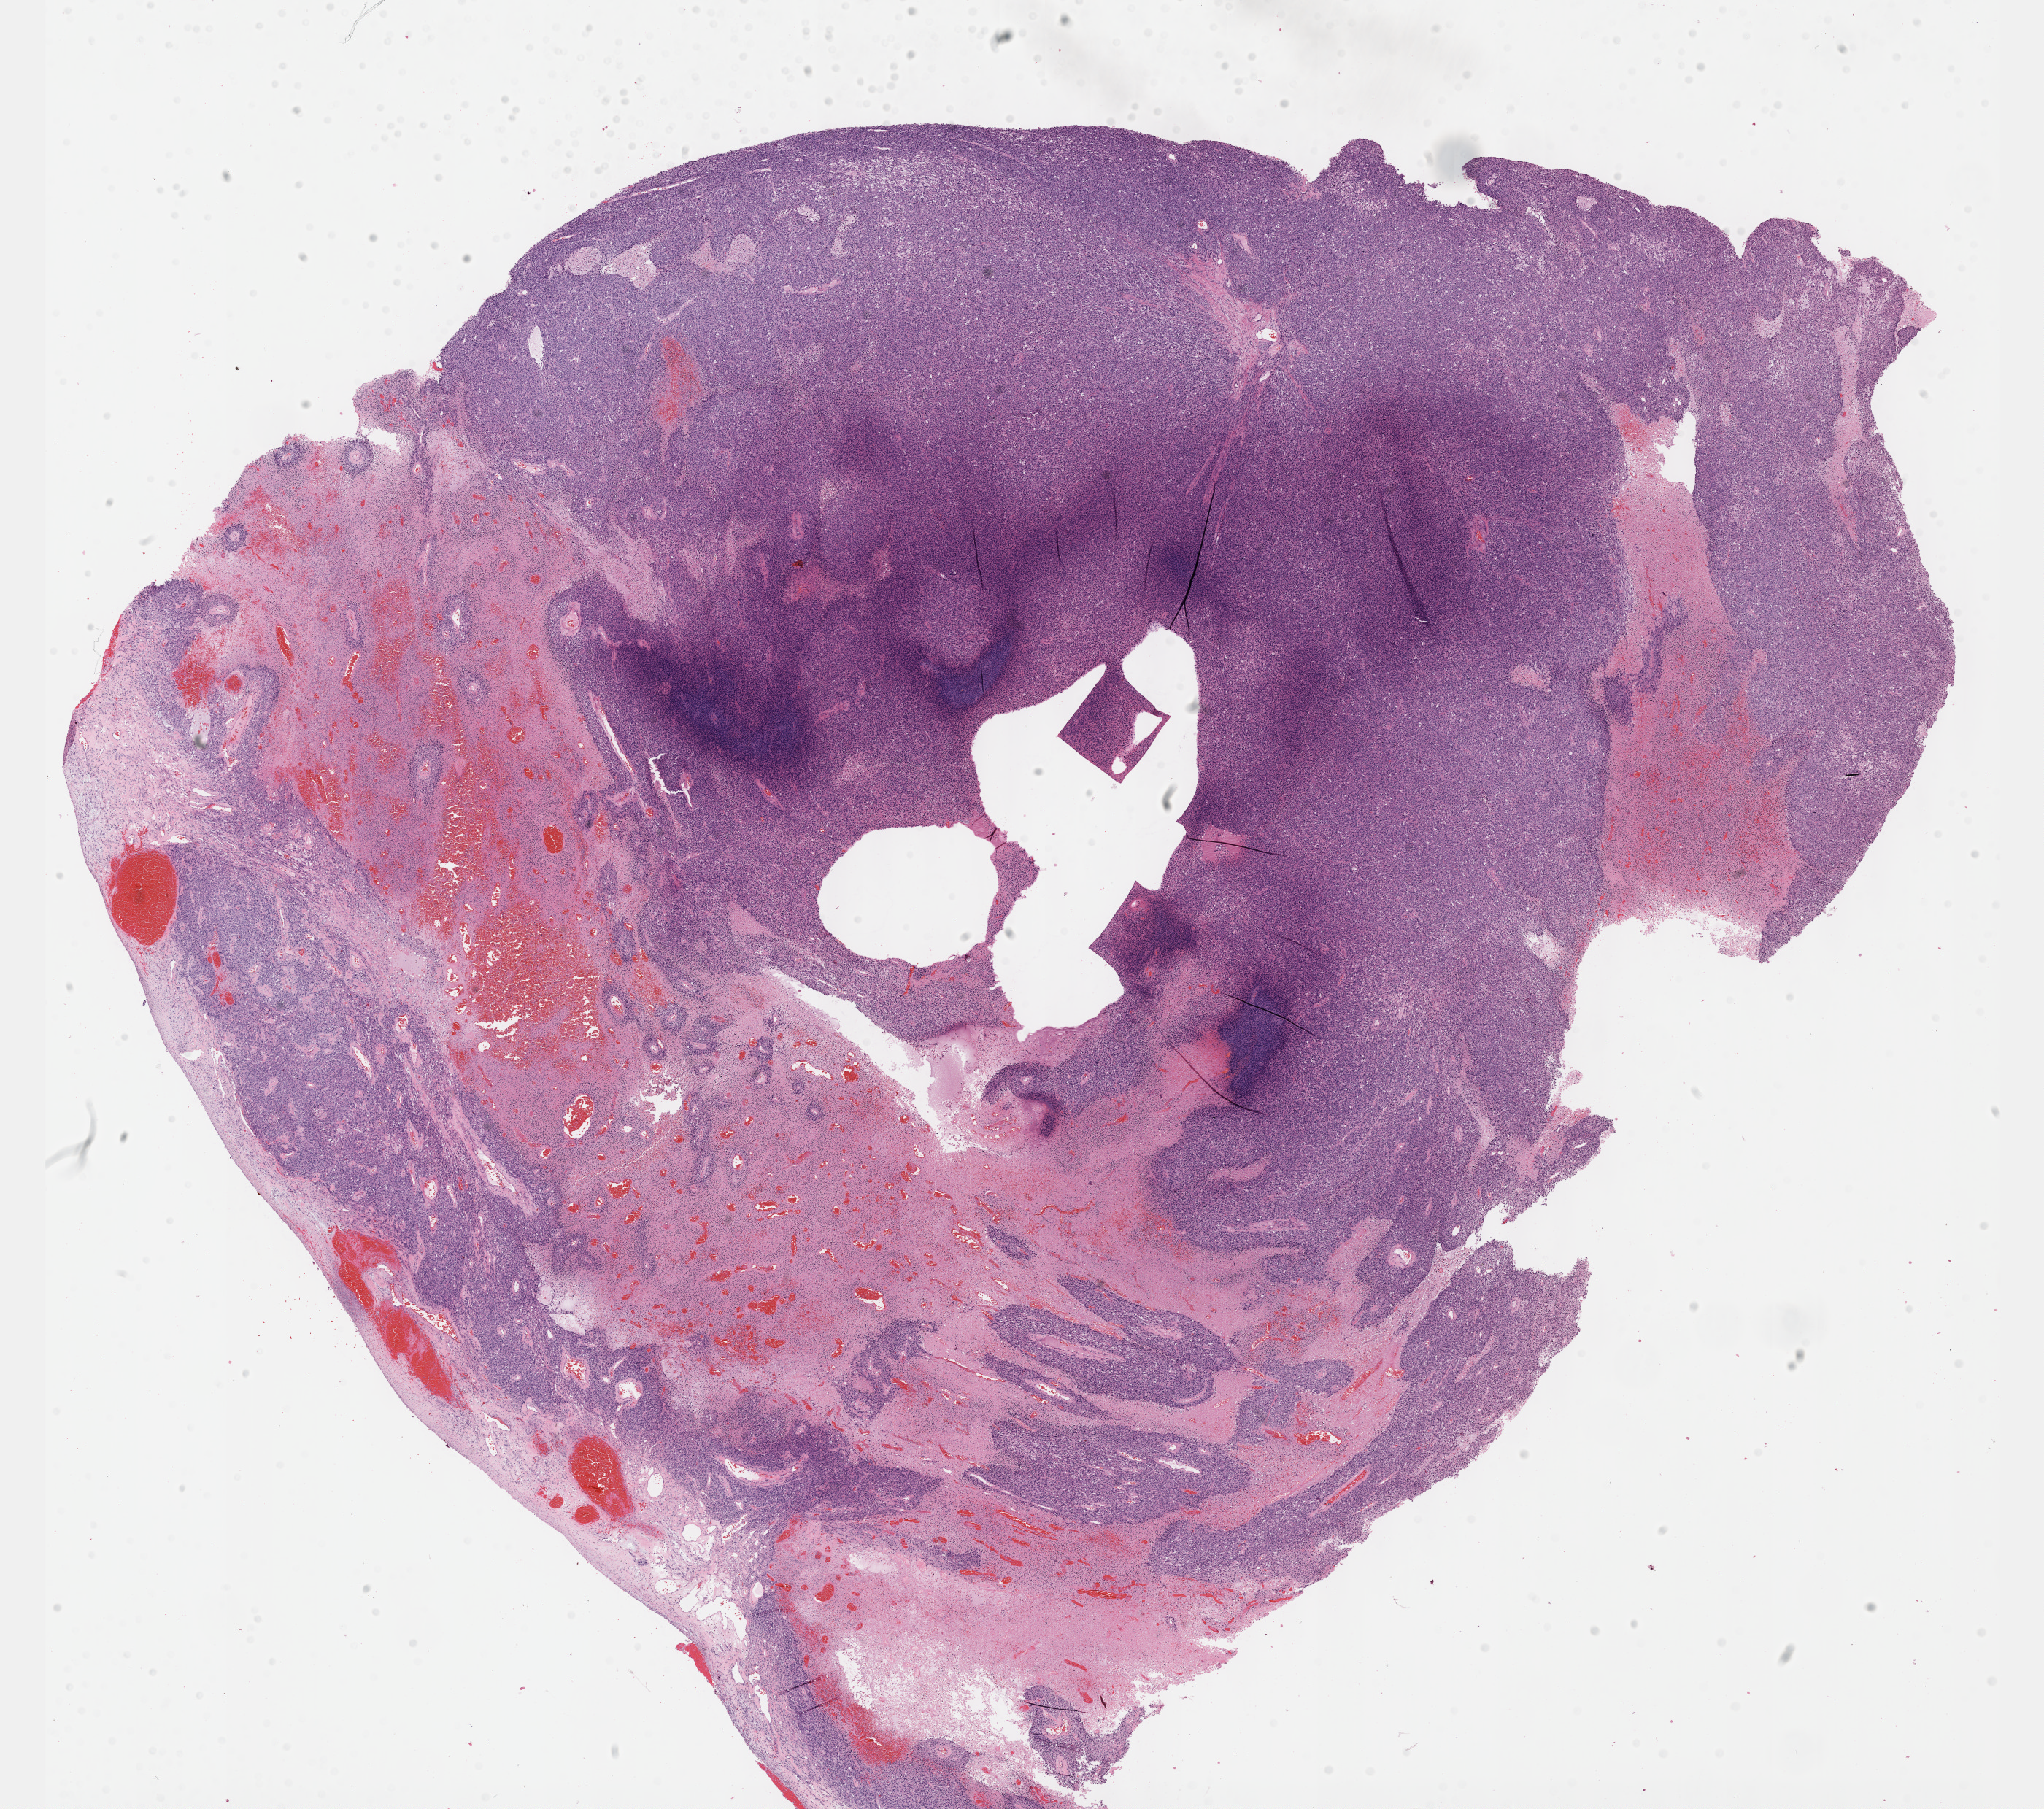
Digitized Hematoxylin and eosin (H&E) stained tissue section (whole slide) — low-resolution overview of the scanned area, about 22.6 x 20.0 mm. Formalin-fixed paraffin-embedded (FFPE) diagnostic section. Sample: primary tumour, uterus. Patient: female, age at initial diagnosis 58 years.
* pathologic diagnosis: Leiomyosarcoma, NOS